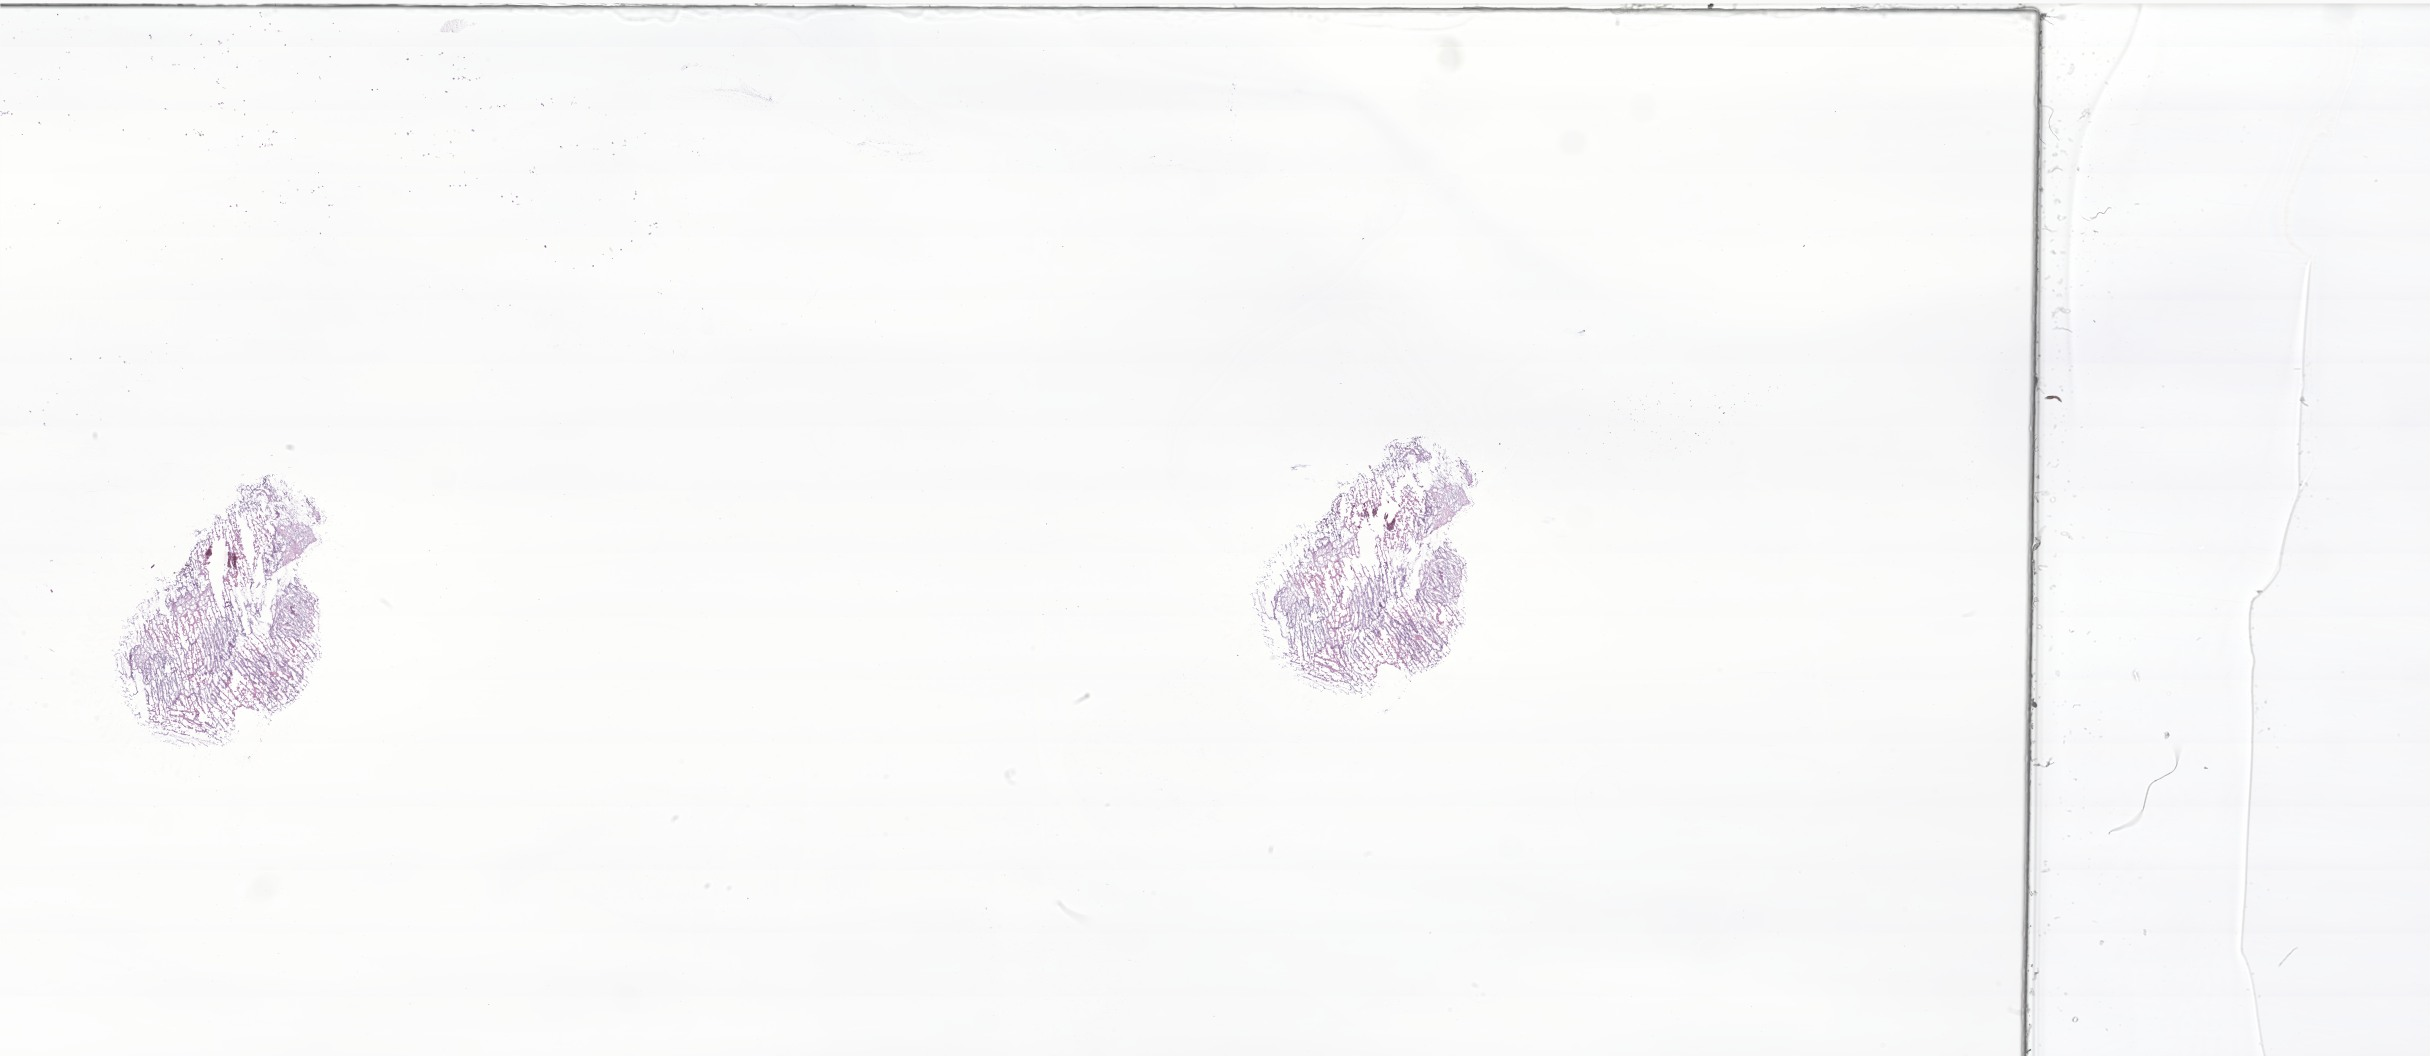
Hematoxylin and eosin (H&E) whole-slide image of tumor tissue from the lower limb — low-resolution overview of the scanned area, about 41.0 x 17.8 mm. Cryosection (OCT / tissue freezing medium). Female patient, age 545 days (about 1.5 years).
- diagnosis: Alveolar rhabdomyosarcoma